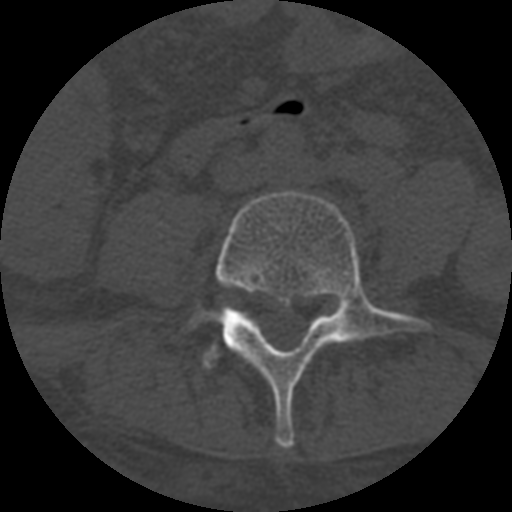
CT including the spine, one axial slice; slice 207 of 708 in the series (ordered by position); one of 3 acquisitions stored at this slice position; bone window (W 1800 / L 400 HU); 1.25 mm slice thickness; 512 × 512 image matrix, field of view 160 × 160 mm. Patient age 55 years. Case-level facts recorded for this patient, not image findings: primary cancer: colon; vertebrae with lytic lesions (as recorded): T12, L1, L5.
Annotated regions visible in this slice (semi-automatic segmentation, software-assisted and operator-edited):
- L4 vertebra: bounding box (x1, y1, x2, y2) in pixels: (186, 191, 430, 449)